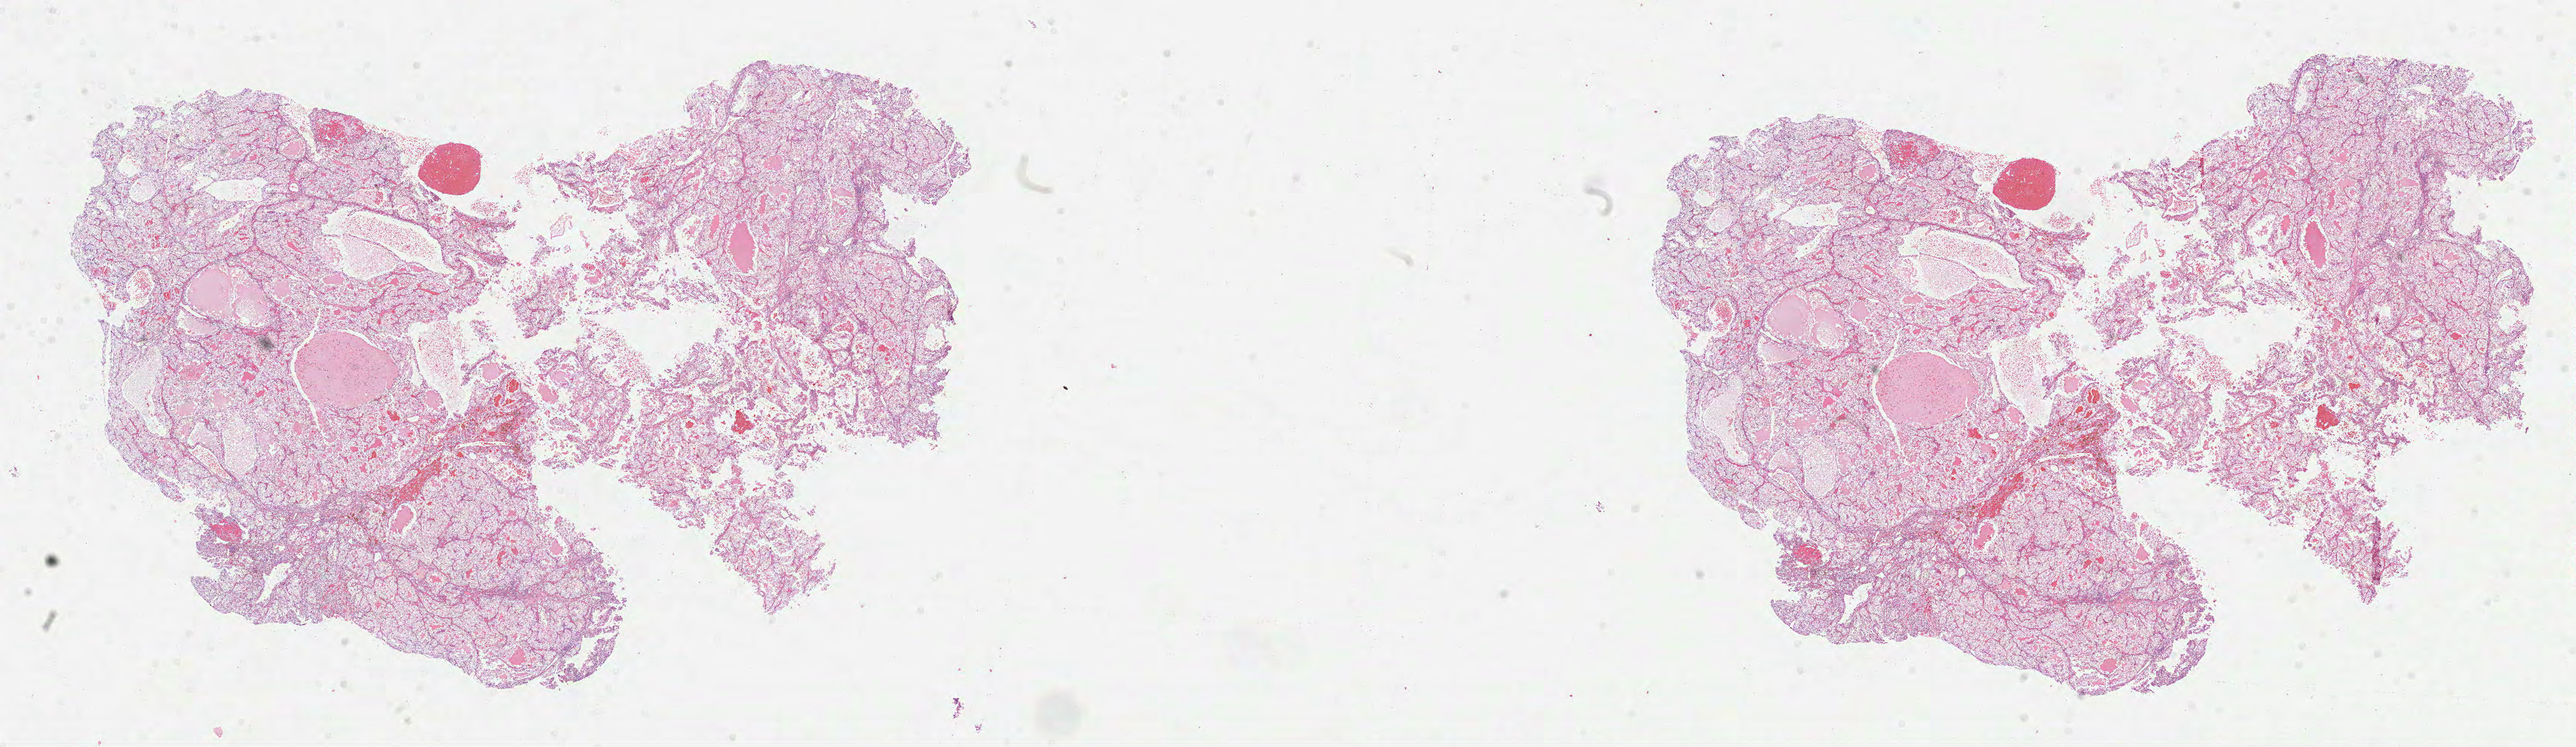
Digitized H&E tissue section (whole slide) — a low-resolution overview of the entire scanned area, about 27.6 x 8.0 mm. Formalin-fixed paraffin-embedded (FFPE) diagnostic section. Sample: primary tumour, kidney. Patient: female, age at initial diagnosis 57 years. Histologic grade: G2 (moderately differentiated).
* pathologic diagnosis: Clear cell adenocarcinoma, NOS
* AJCC pathologic stage: I